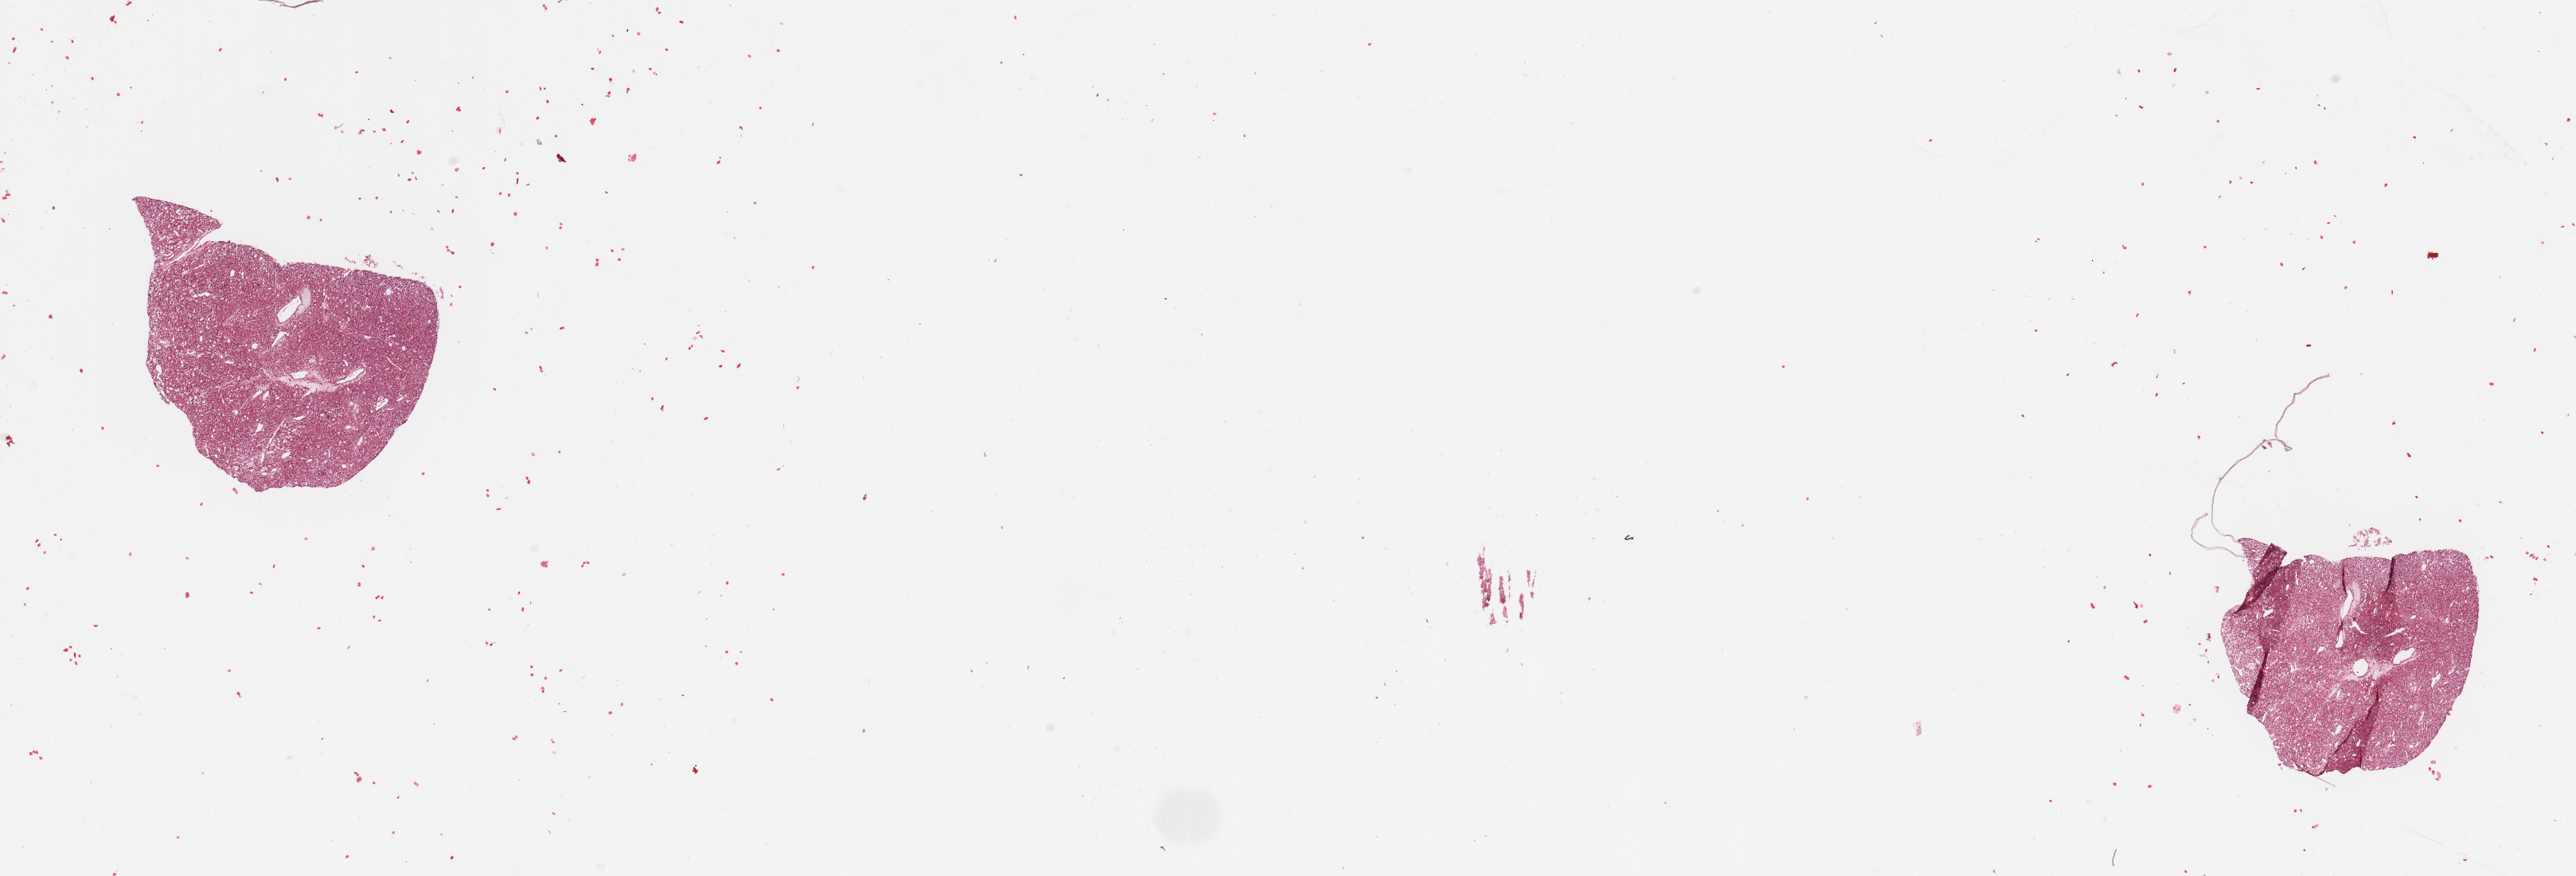
Hematoxylin and eosin (H&E) stained whole-slide image, whole scanned area (about 25.6 x 8.7 mm) shown as a low-resolution overview; tumour tissue sample, sampled site: kidney. Male, 65 y/o. Histologic grade: G1 (well differentiated). Pathologist review of this section (percent, as recorded): tumour nuclei 95%, necrosis 0%.
AJCC pathologic stage: I. Primary tumour site (as recorded): upper pole. Diagnosis: Renal cell carcinoma, NOS.